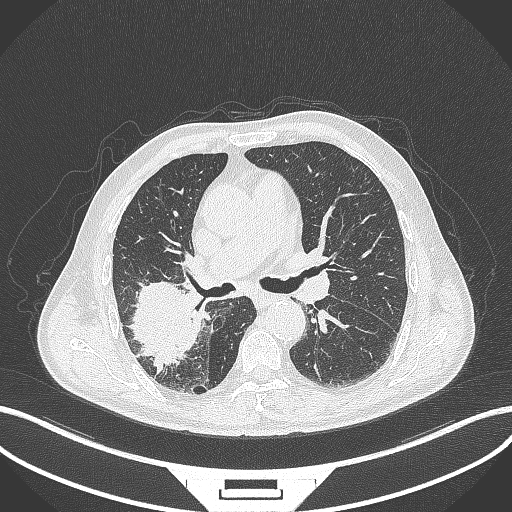
Chest CT, one axial slice. Position 240 of 429 along the scan axis. Reconstruction kernel B70f. 120 kVp. Lung window (W 1500 / L -600 HU). 512 × 512 image matrix, field of view 400 × 400 mm. Patient: male, 72 years. From the clinical record (not read from this slice): clinical TNM (as recorded): T3 N2 M0.
Outlined on this slice (bounding box drawn by a radiologist):
- lung tumour (recorded histology: adenocarcinoma): box from (x=124, y=278) to (x=203, y=373) px